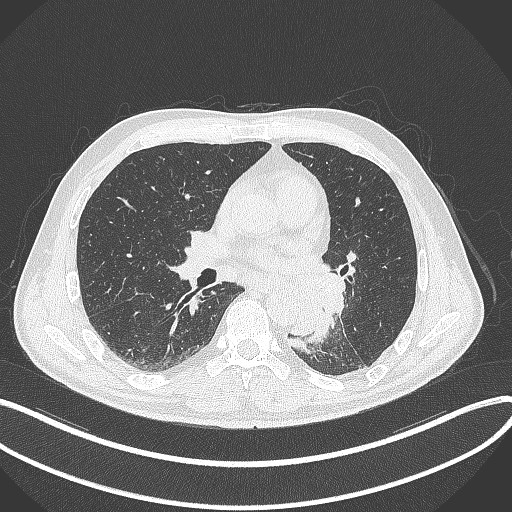
Chest CT, one axial slice. Slice 169 of 329 in the series (ordered by position). Reconstruction kernel B70f. 120 kVp. Lung window (W 1500 / L -600 HU). 1 mm slice thickness. 512 × 512 image matrix, field of view 400 × 400 mm. Patient: male, 59 years. From the clinical record (not read from this slice): clinical TNM (as recorded): T2a N2 M0.
Structures marked on this image (rectangle marked by the reading radiologist):
- lung tumour (recorded histology: squamous cell carcinoma): bounding box [x1, y1, x2, y2] px = [291, 268, 343, 344]